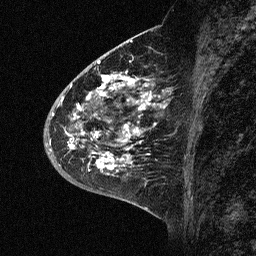
Breast MRI (dynamic contrast-enhanced), one sagittal slice. Dynamic contrast-enhanced study with each time point stored as its own series, time point 2 of 3 at this slice position (early post-contrast, ordered by acquisition time). 1.5 T. TE 4.5 ms, TR 11 ms. 256 × 256 image matrix, field of view 200 × 200 mm. Female patient, age 46 years. From the clinical record (not read from this slice): setting: breast cancer imaged before/during neoadjuvant chemotherapy; receptor status: HER2-positive.
Outlined on this slice (semi-automatic segmentation, software-assisted and operator-edited):
- analysis volume of interest (the breast-tissue region the enhancement analysis was run in; not a lesion): bounding box <43,72,176,177> (left, top, right, bottom; pixels)
- tumour enhancement mask (voxels above the 90 % enhancement threshold inside the analysis volume of interest): <59,72,158,173>